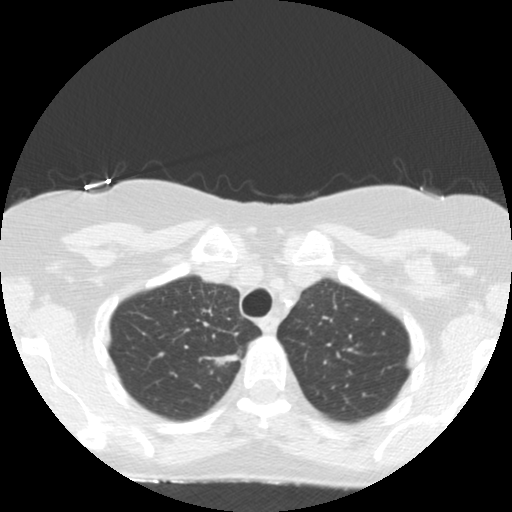
Axial slice from a low-dose chest CT screening exam. Baseline annual screen. Lung window (W 1500 / L -600 HU). 2.5 mm slice thickness. Standard (soft-tissue) reconstruction kernel (STANDARD). Slice 30 of 155 in the series. Female participant, aged 67 years at enrolment.
Expert reader's lesion annotation, box from (x=195, y=338) to (x=253, y=386) px. The exam's reader record, not a measurement of the box and not confirmed to be the same lesion: non-calcified nodule or mass ≥4 mm, right upper lobe, 16 × 7 mm, poorly defined margins, mixed attenuation. Official screen result: positive, change unspecified: nodule(s) >= 4 mm or enlarging nodule(s), mass(es), or other non-specific abnormalities suspicious for lung cancer.